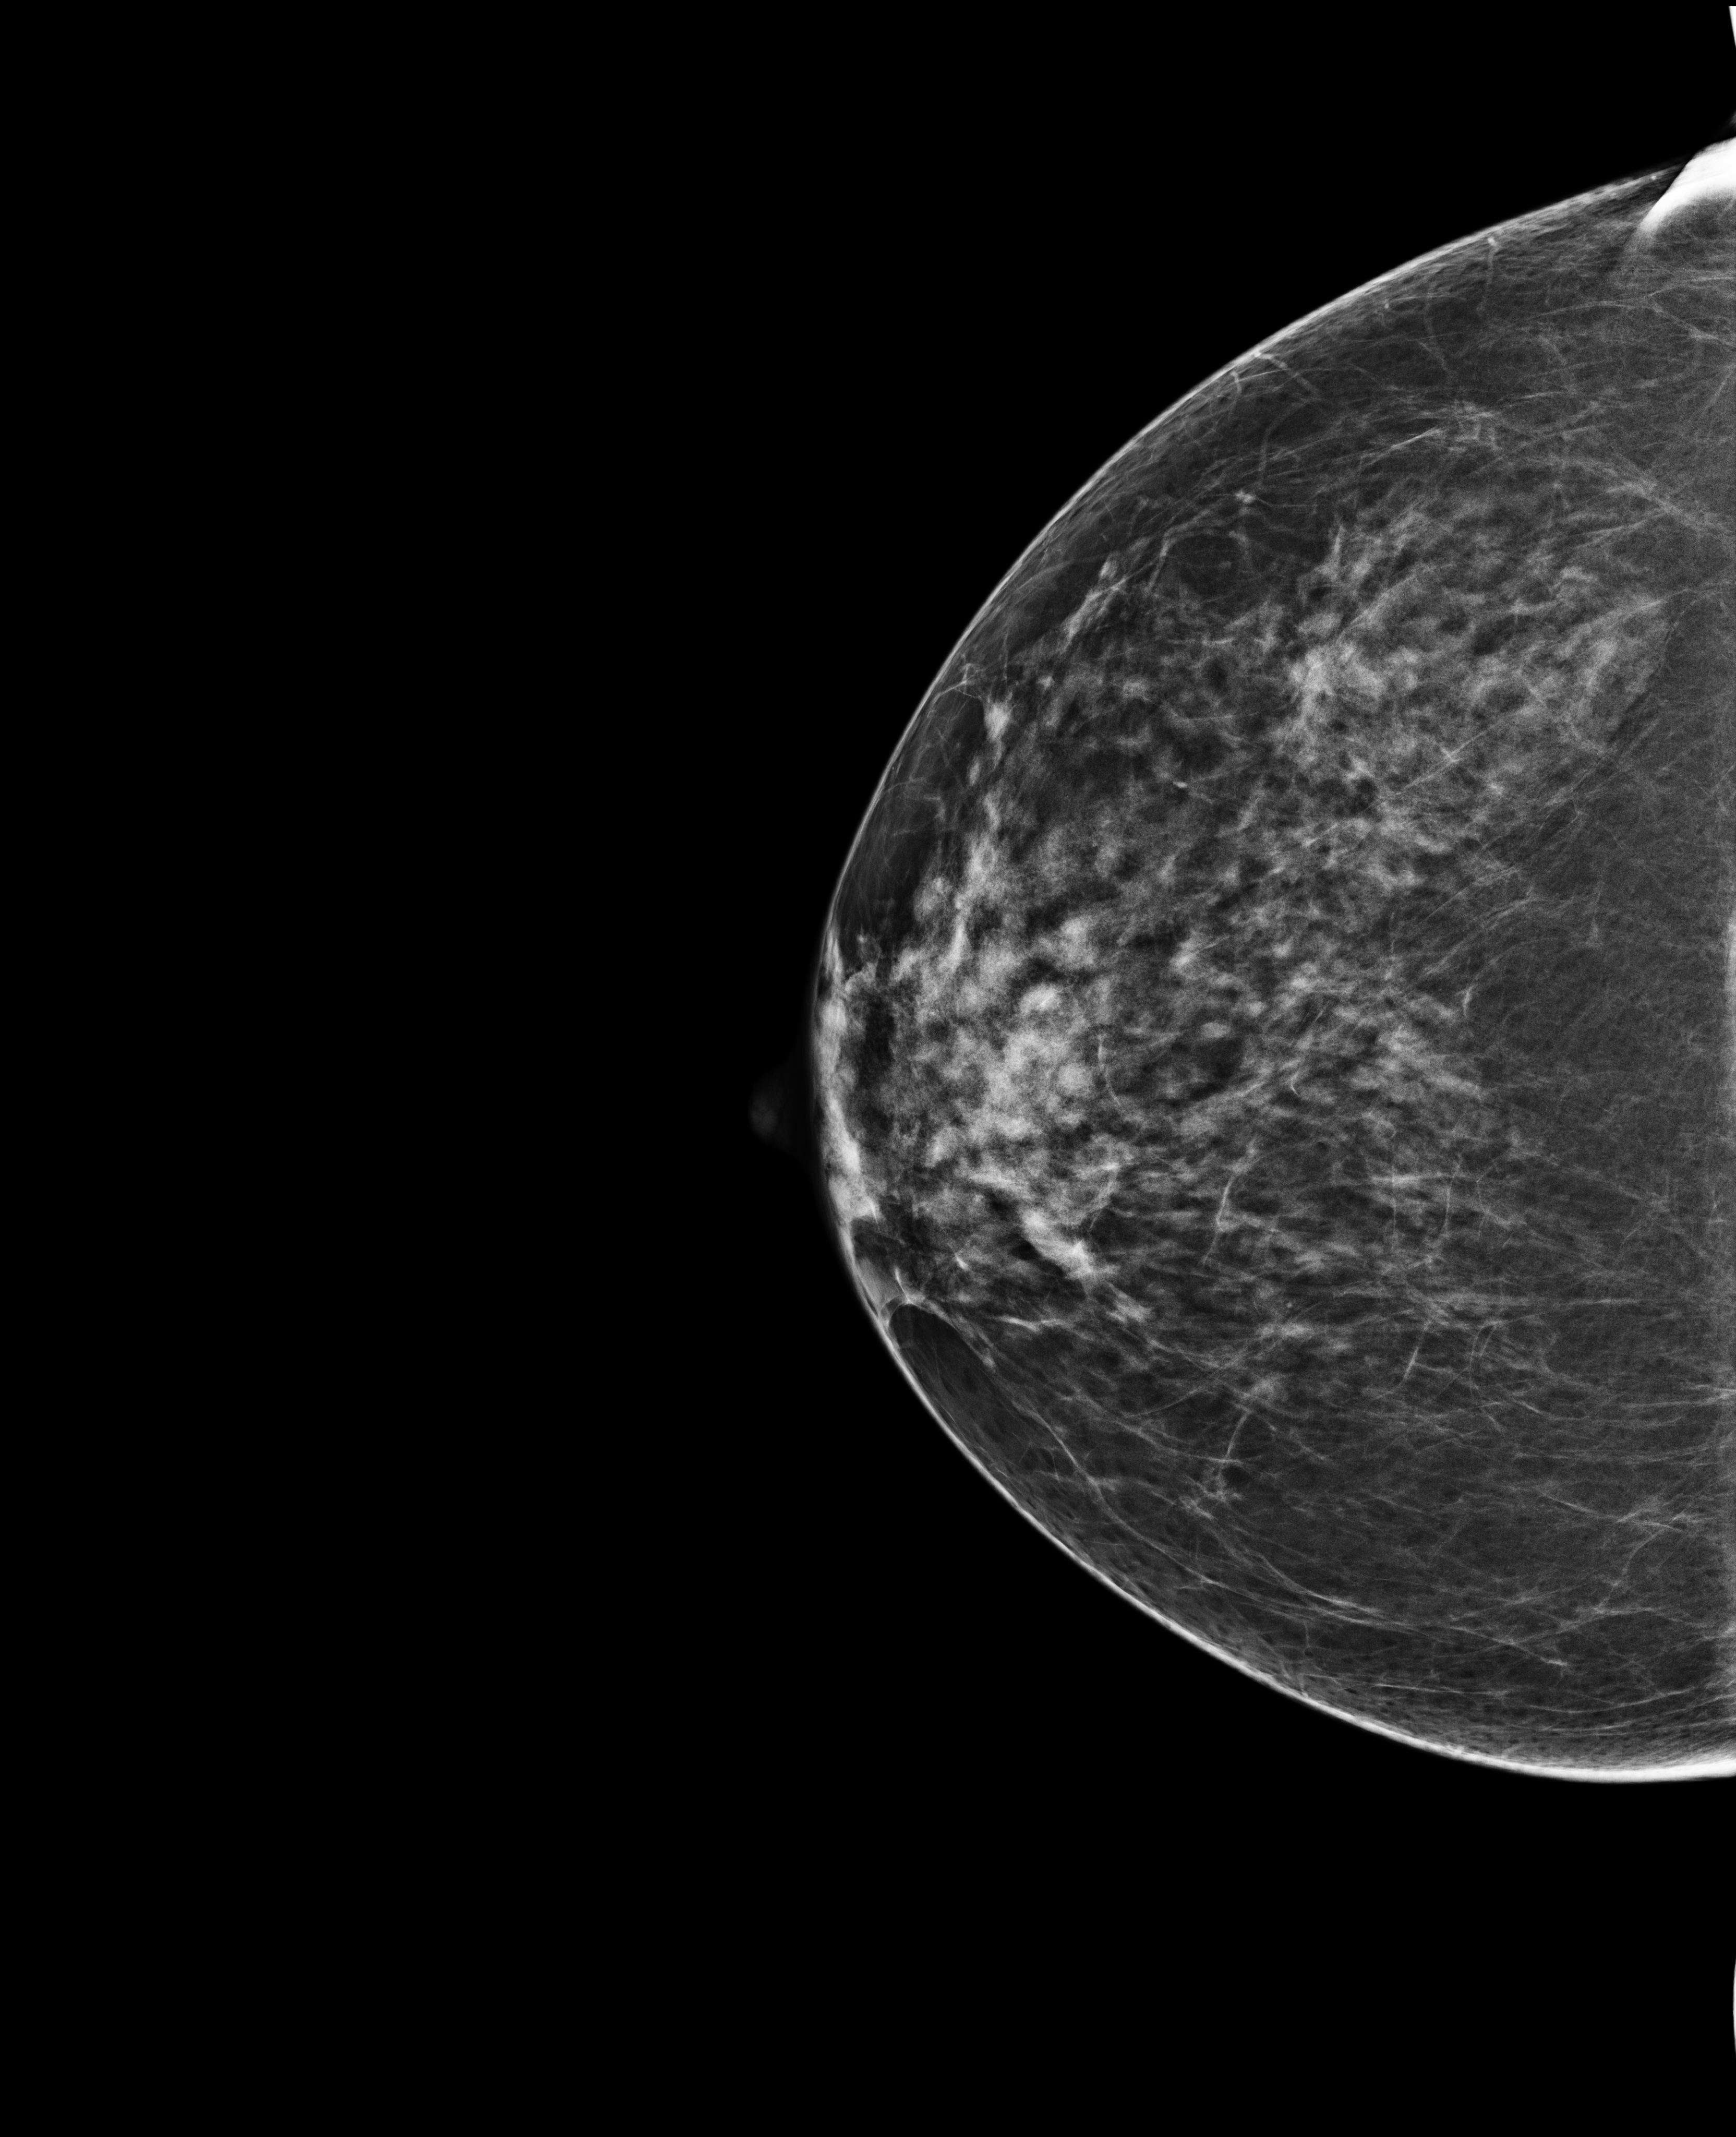
Digital mammogram (FFDM), right breast, craniocaudal (CC) view, annual screening mammography examination, compressed breast thickness 75 mm. Patient: female, 52 years.
- breast density at the screening exam (both breasts): heterogeneously dense (BI-RADS density category c)
- final BI-RADS category for the screening round (tomosynthesis exam, both breasts): category 1
- recall: no recall after this screen